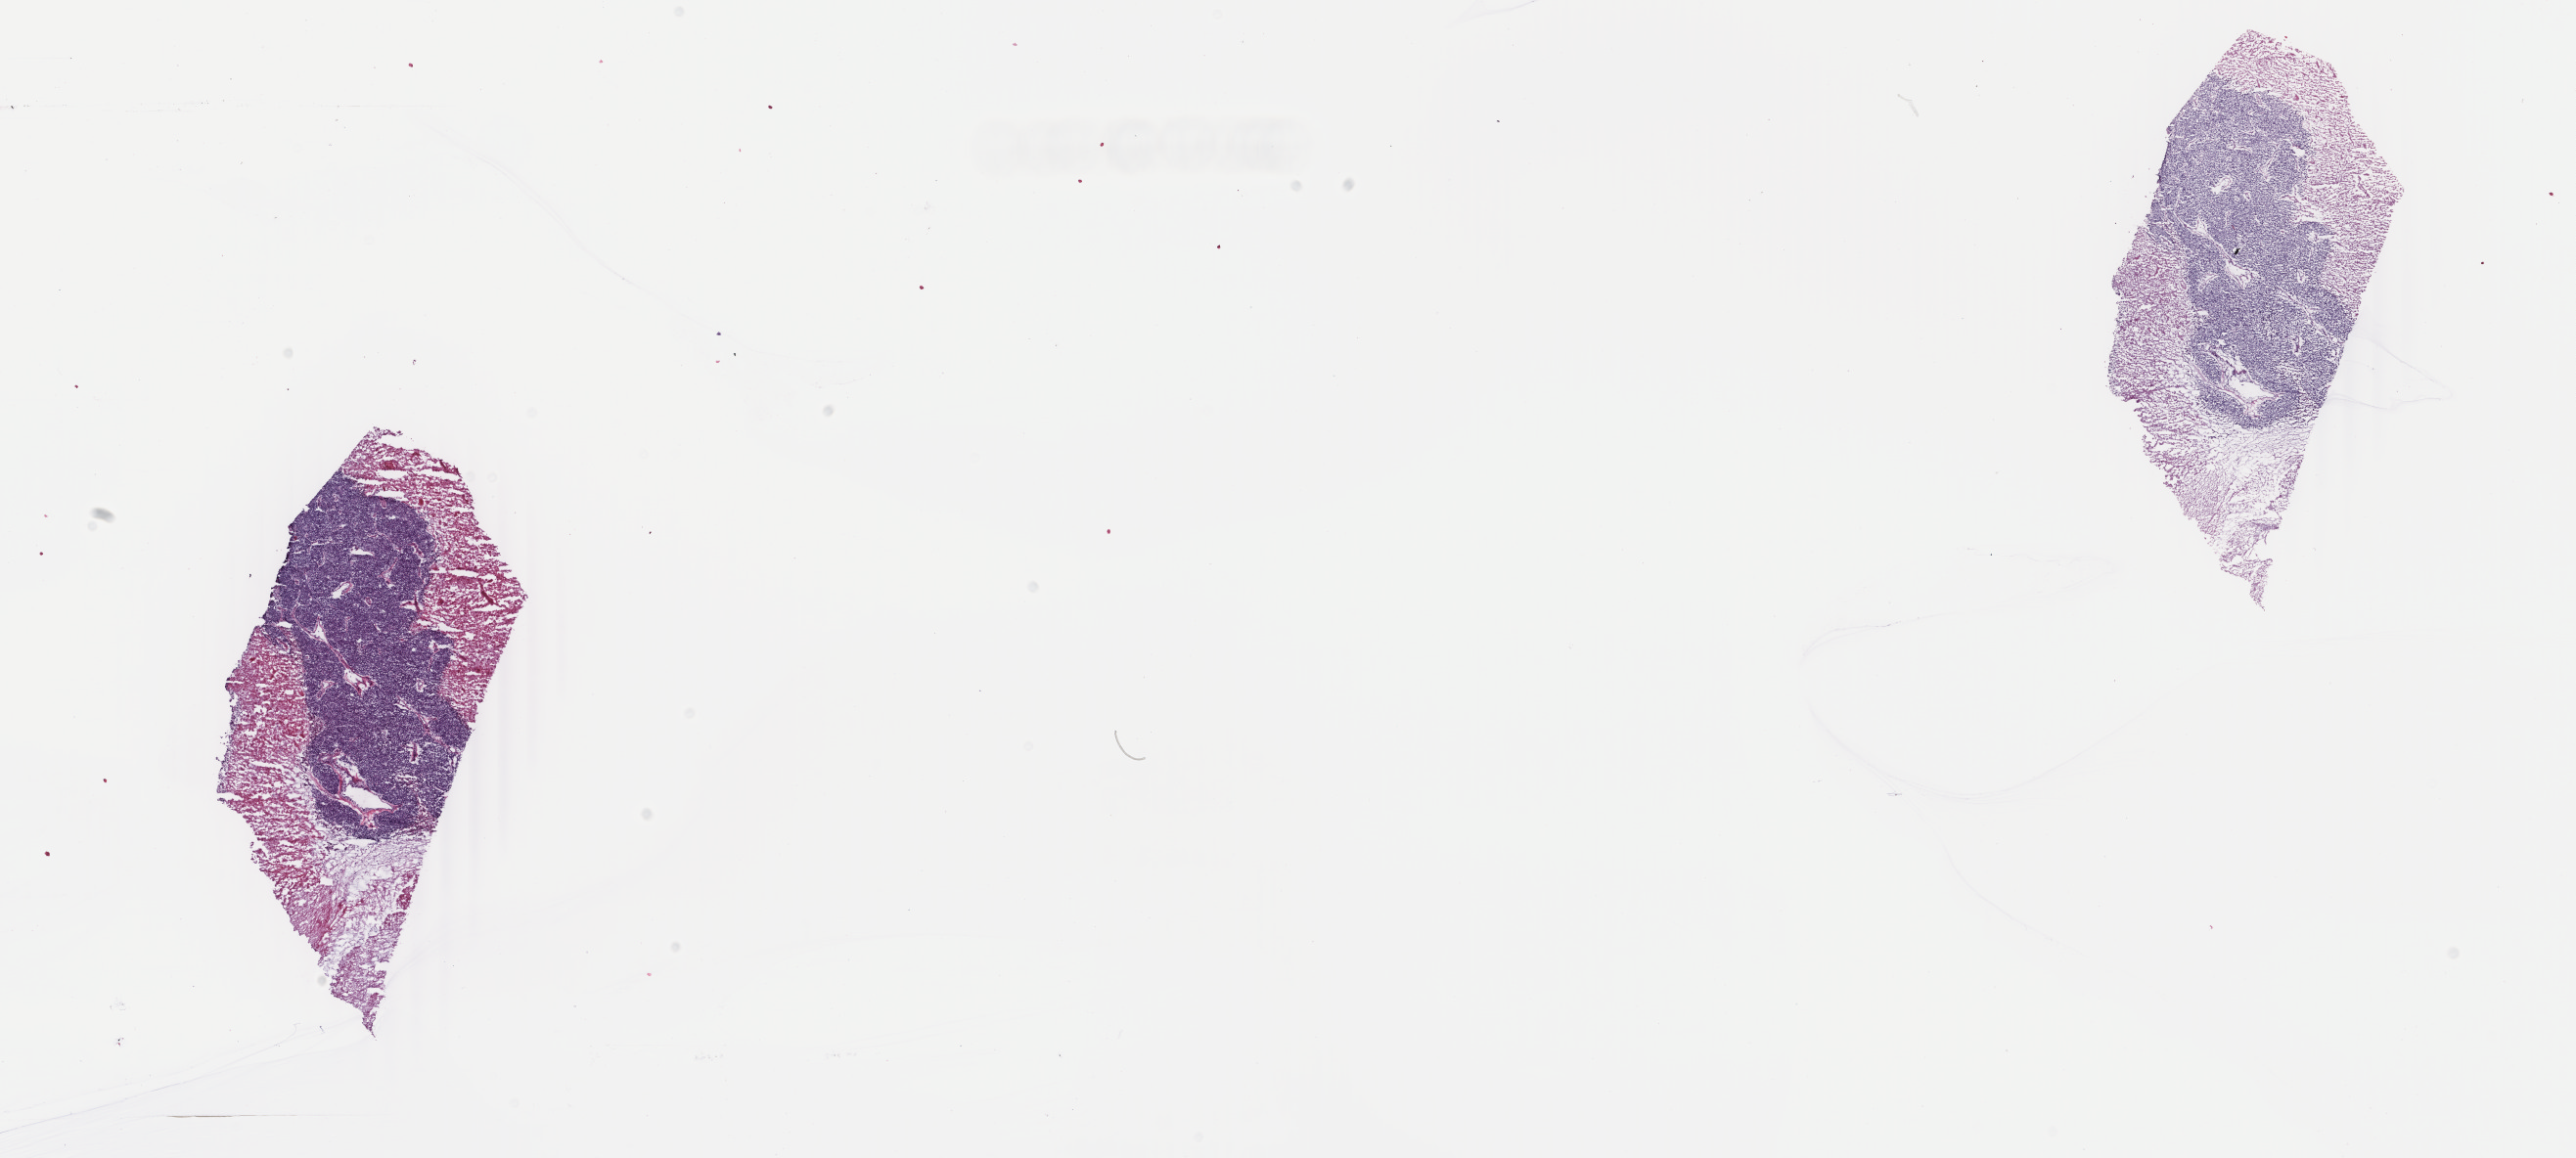
Hematoxylin and eosin (H&E) stained whole-slide image, a low-resolution overview of the entire scanned area, about 20.9 x 9.4 mm (slide scanned at 40x). Frozen section from the top of the tissue portion. Uterus, primary tumour sample. Patient: female, age at initial diagnosis 66 years. Histologic grade: G3 (poorly differentiated). Composition of this section per pathologist review: tumour cells 70%, tumour nuclei 70%, normal cells 0%, stromal cells 10%, necrosis 20%. Inflammatory infiltration, as recorded: lymphocyte infiltration 40%, monocyte infiltration 20%, neutrophil infiltration 30%.
- FIGO stage: IIIA
- lymph nodes positive (case pathology): 0 of 7 examined
- histologic diagnosis: Endometrioid adenocarcinoma, NOS (endometrium)